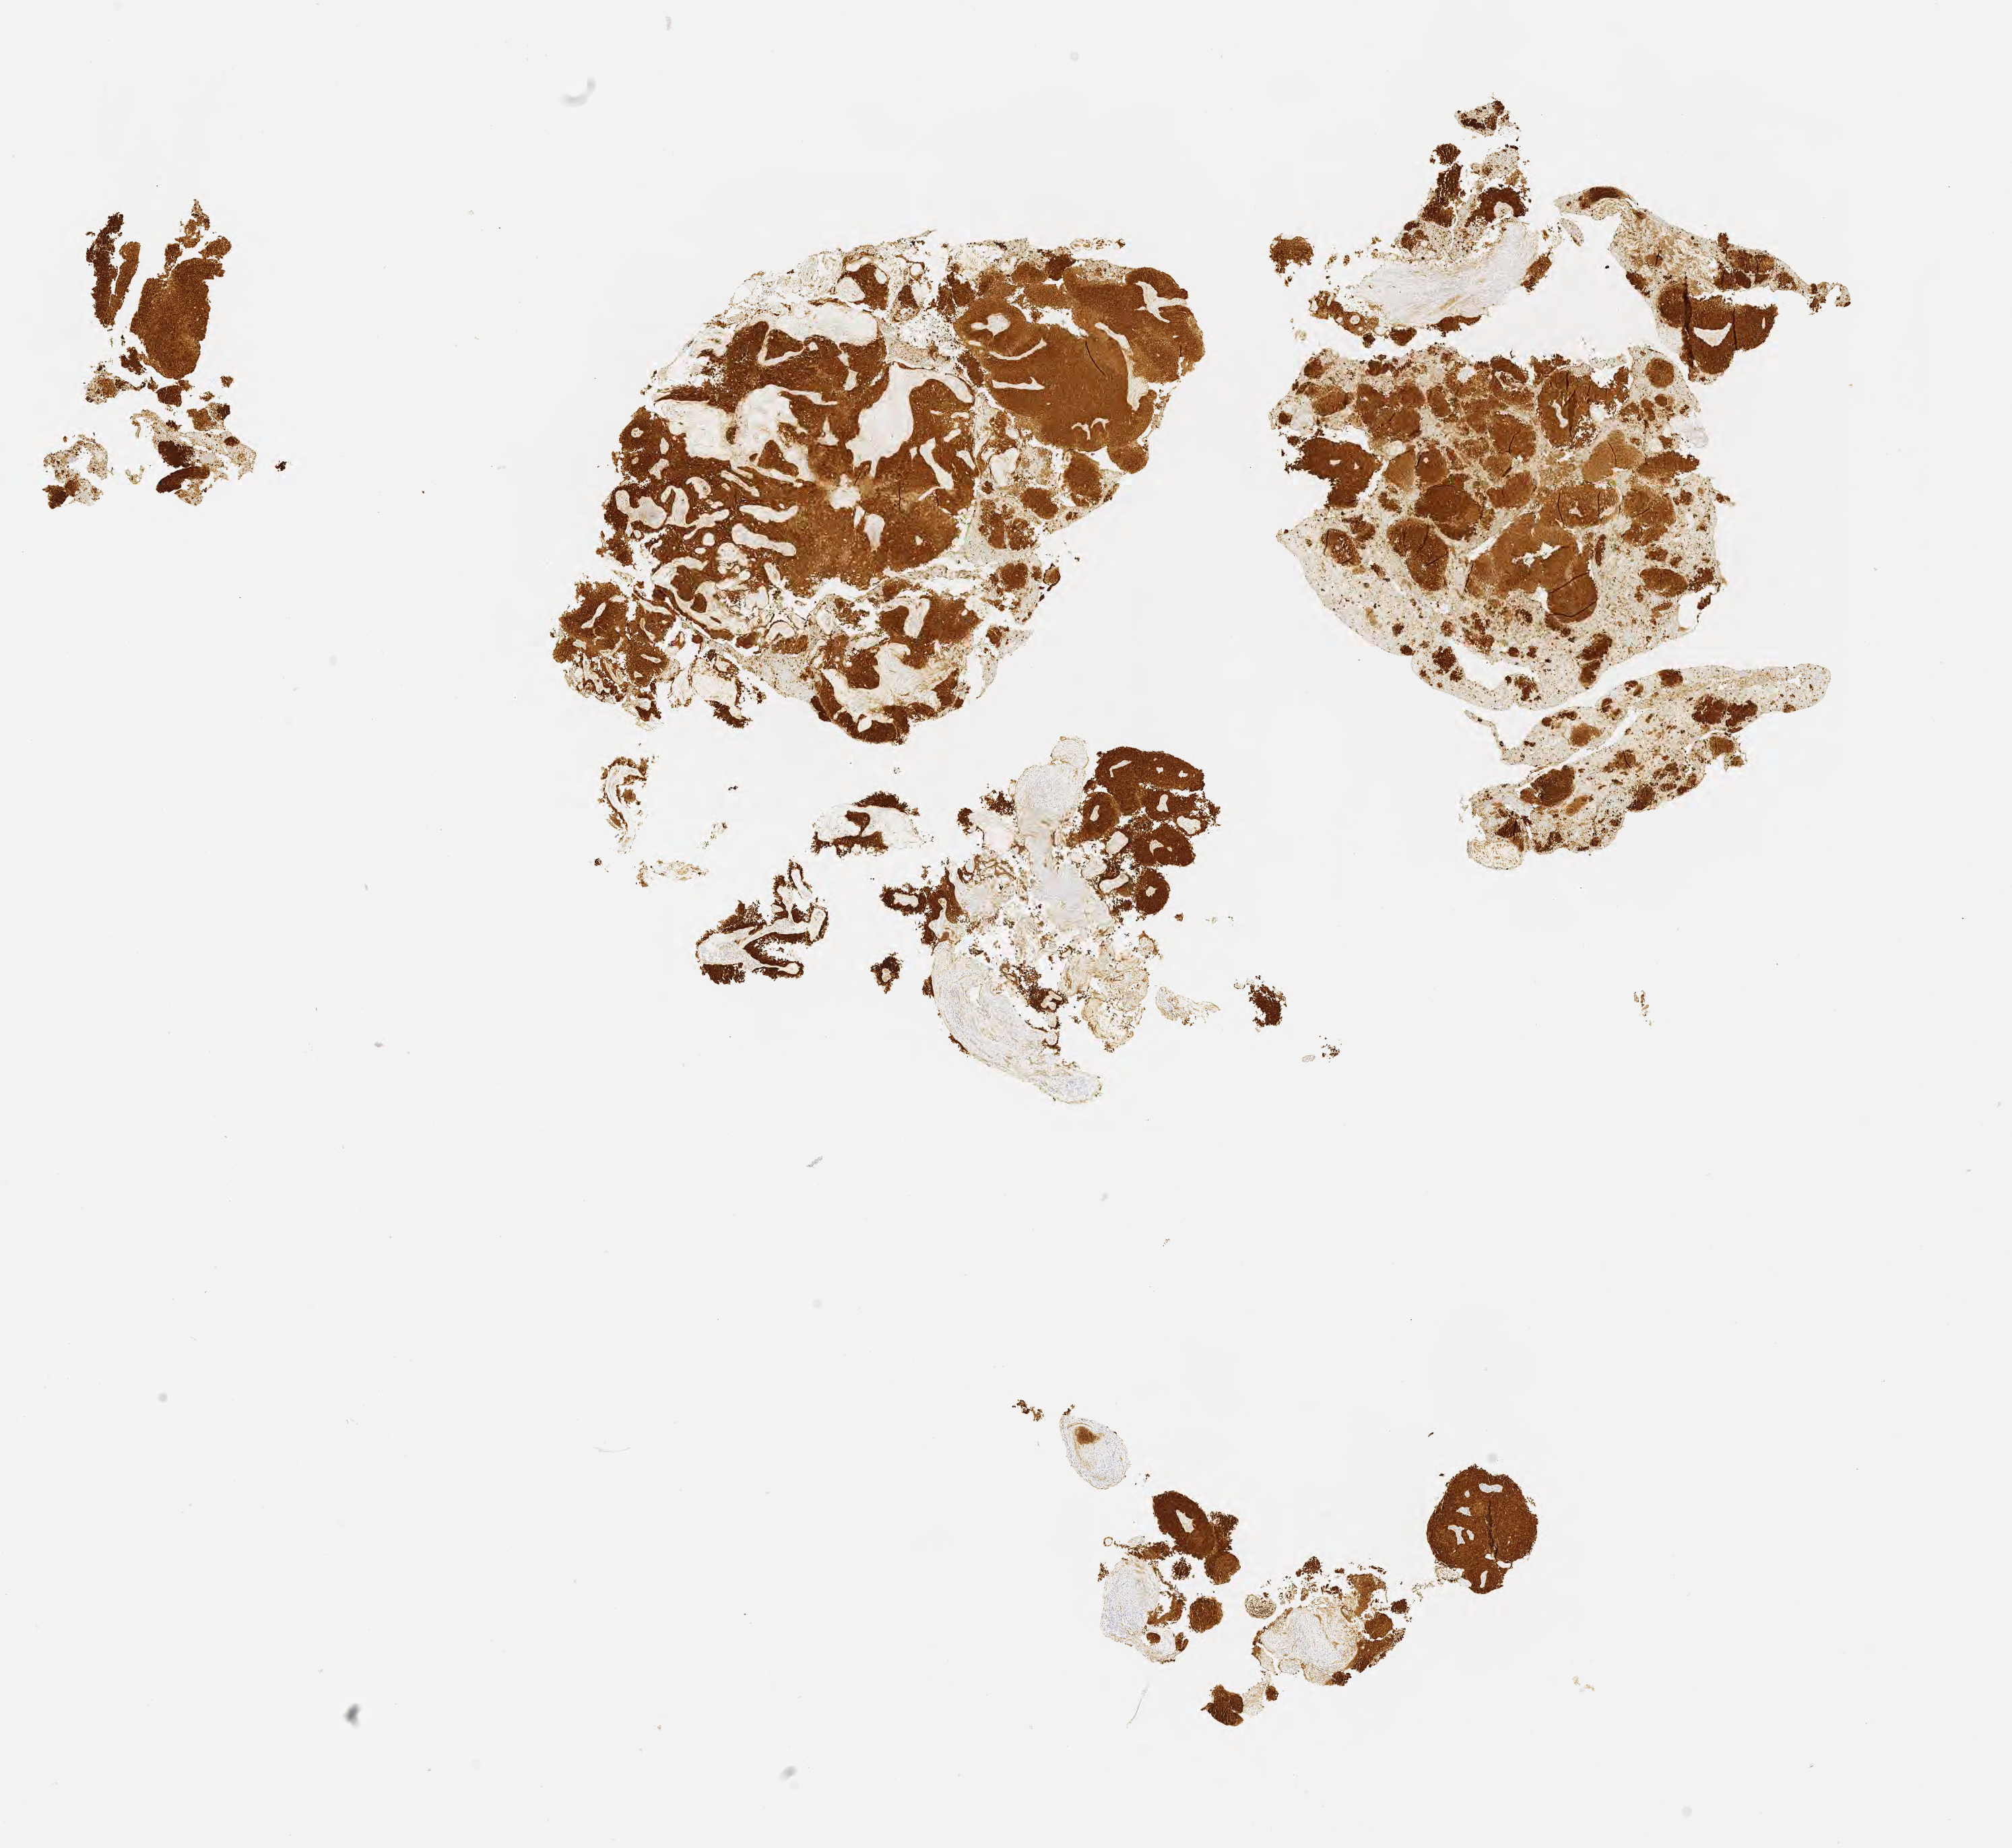
Whole-slide image, immunohistochemical stain for p16 (p16INK4a) — a low-resolution overview of the entire scanned area, about 12.1 x 11.1 mm. Tumor tissue. Anatomic site: cervix. Female patient, age 44 years.
Histologic diagnosis: Squamous cell carcinoma, large cell, nonkeratinizing, NOS.